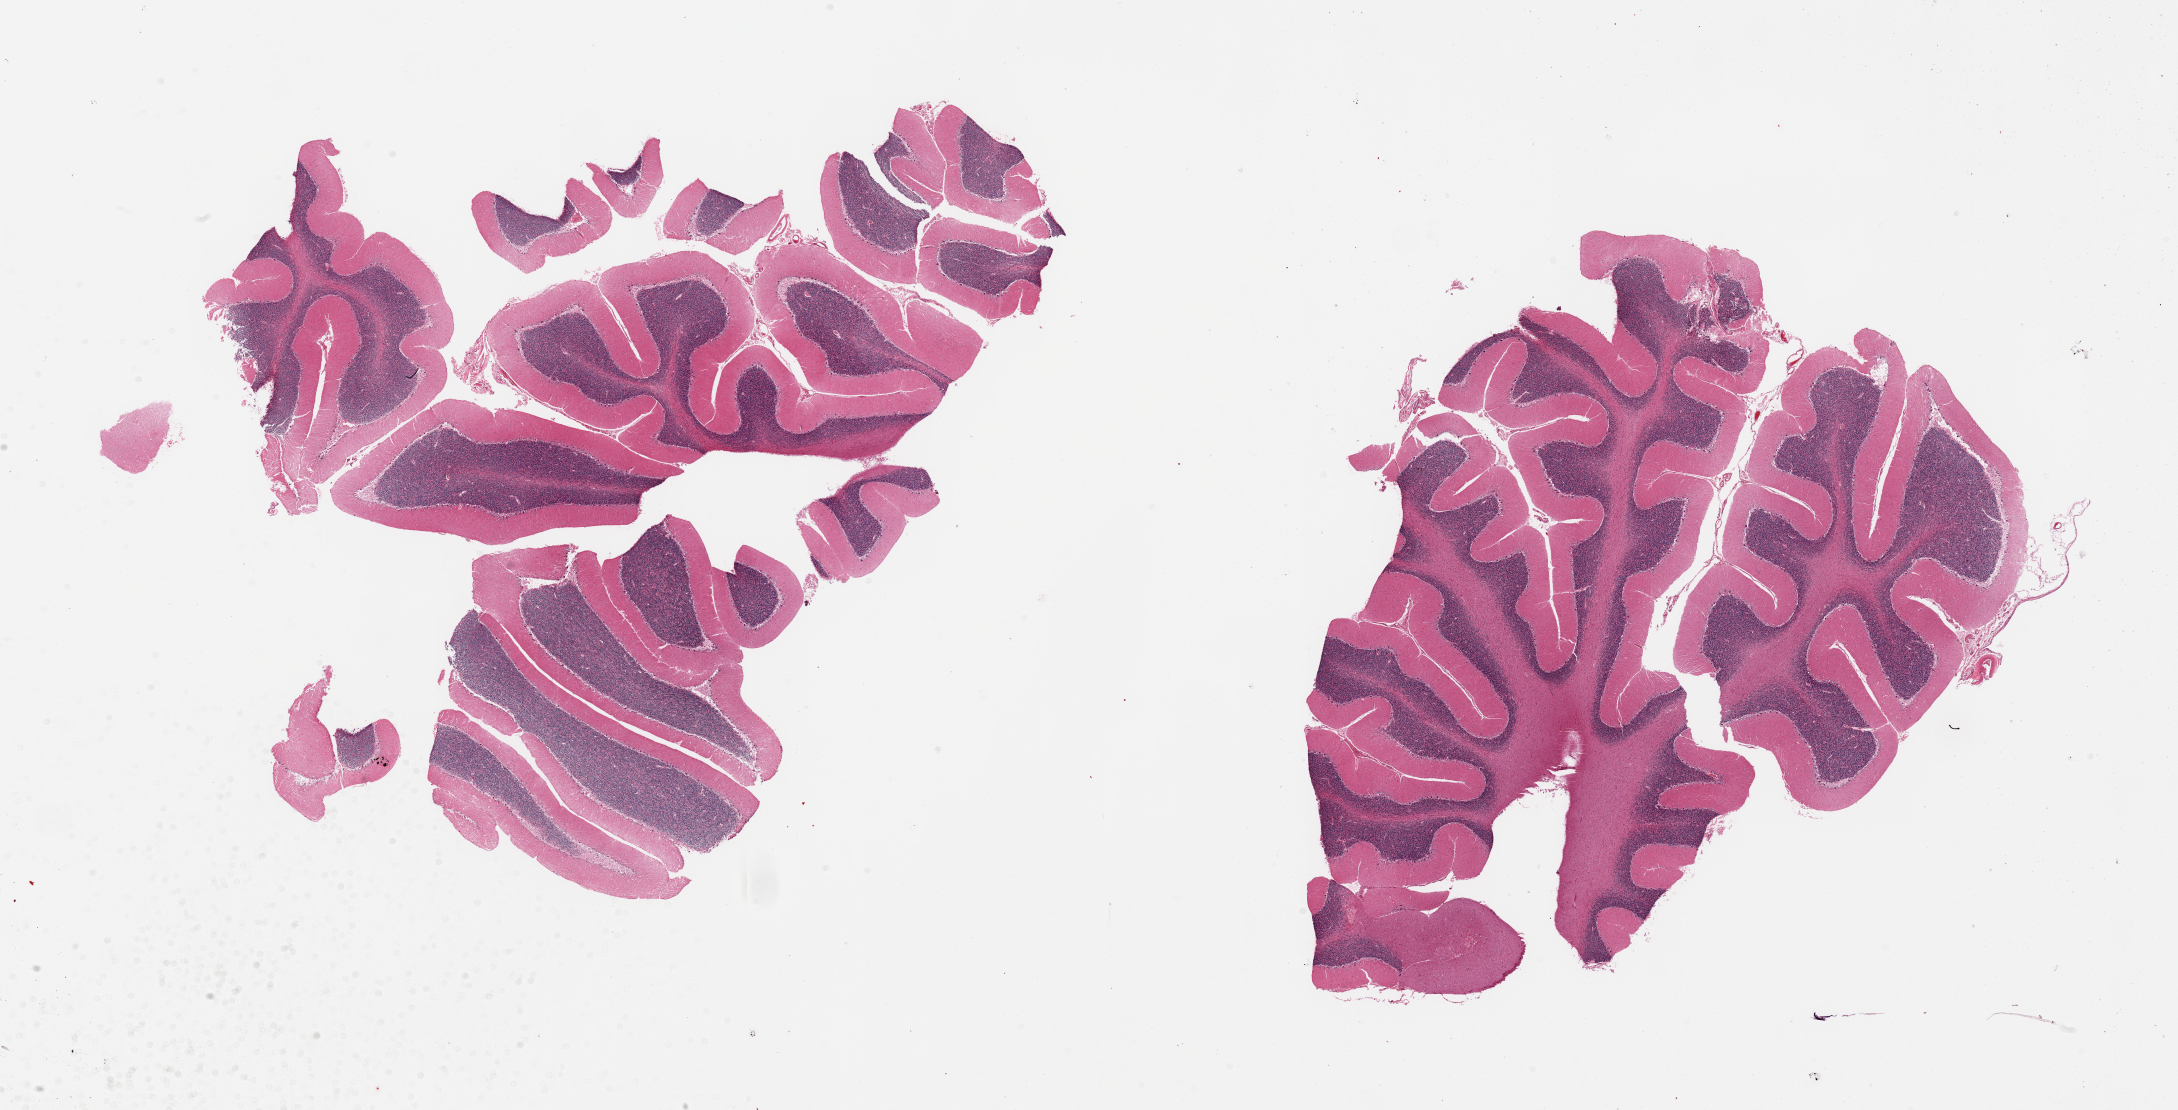
Hematoxylin and eosin (H&E) whole-slide image, brightfield — whole scanned area (about 34.5 x 17.6 mm, slide scanned at 20x) shown as a low-resolution overview. PAXgene-fixed, paraffin-embedded tissue. Section of cerebellum (target tissue). Tissue donor sample.
Reviewer comment on this tissue sample: 2 pieces, no abnormalities.